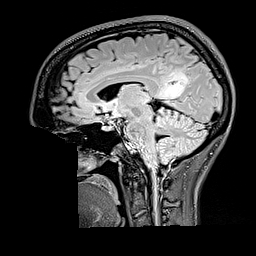
Brain MRI from a brain-tumour surgery series, one sagittal slice; slice 92 of 176 in the series (ordered by position); T2 FLAIR; 1 mm slice thickness; 256 × 256 image matrix, field of view 256 × 256 mm. Case-level facts recorded for this patient, not image findings: histopathology: Oligodendroglioma; WHO grade: 2; IDH mutation: yes; tumour location: Right Parietal.
Outlined on this slice (manually delineated by an expert):
- tumour: box from (x=159, y=69) to (x=189, y=101) px